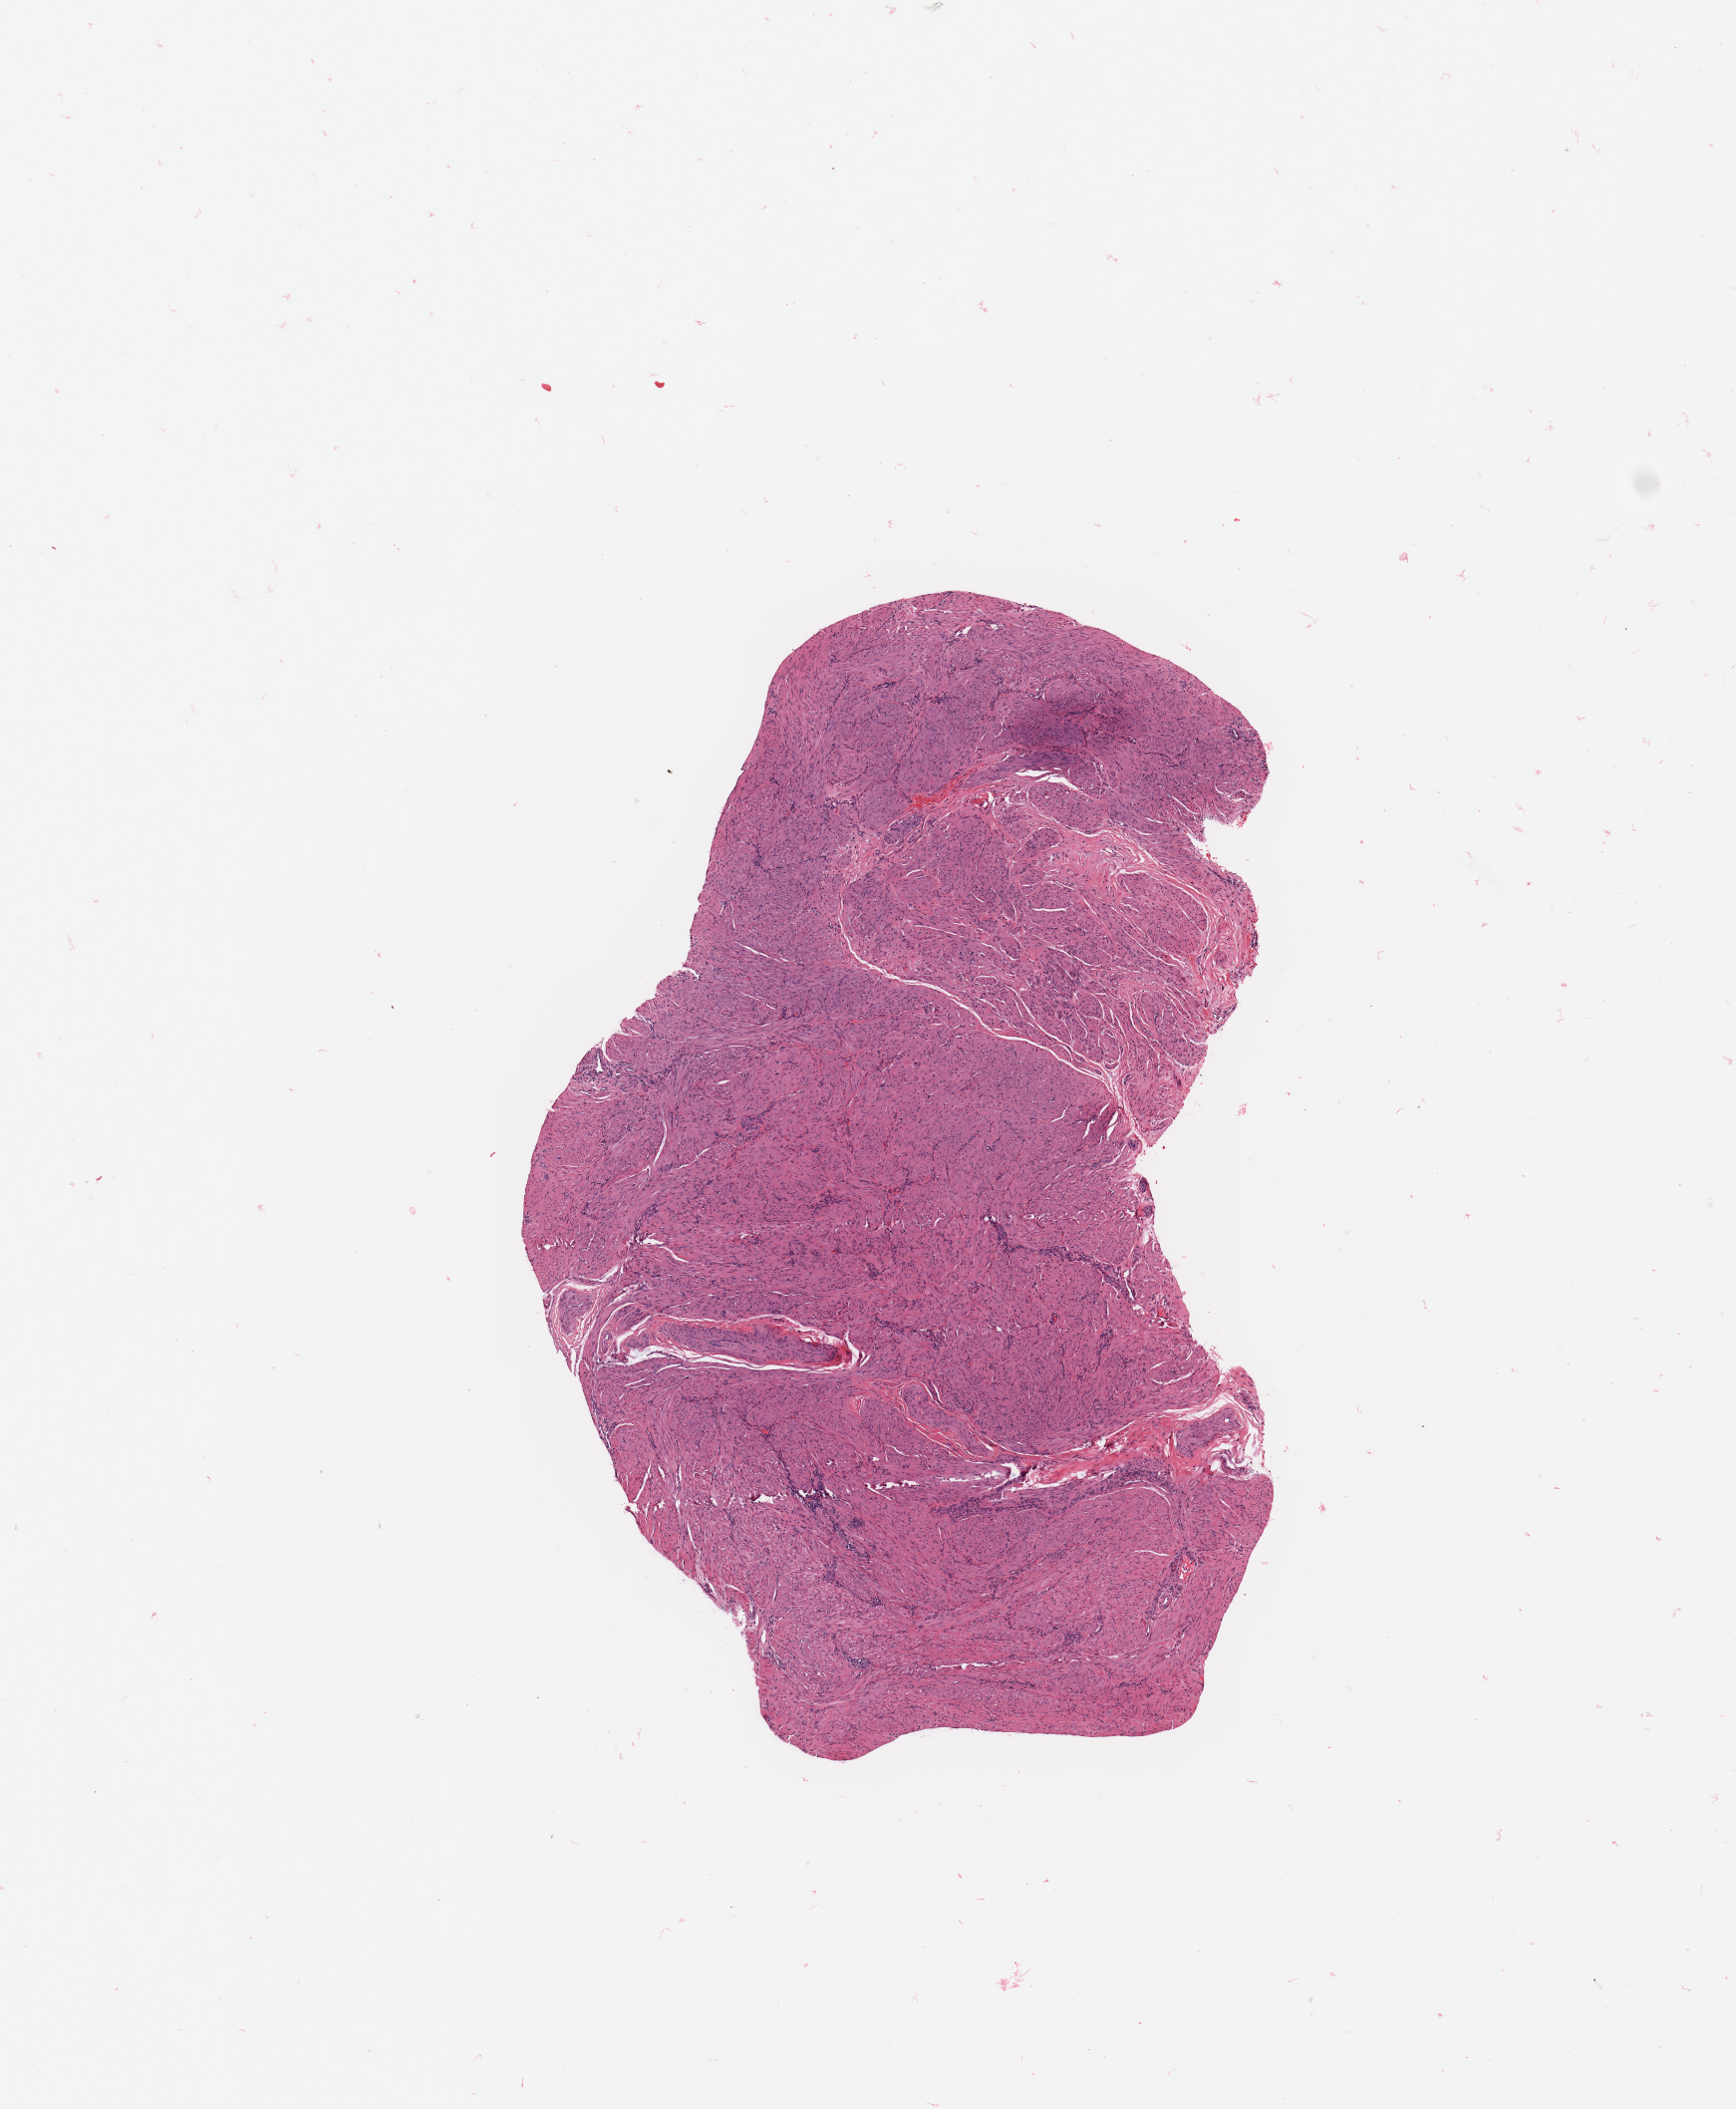
H&E-stained whole-slide image, whole scanned area (about 6.9 x 8.4 mm, slide scanned at 20x) shown as a low-resolution overview; normal (non-tumour) tissue sample, uterus. Female, 56 y/o.
This section: normal (non-tumour) tissue from the same patient. Patient diagnosis: Endometrioid adenocarcinoma, NOS.